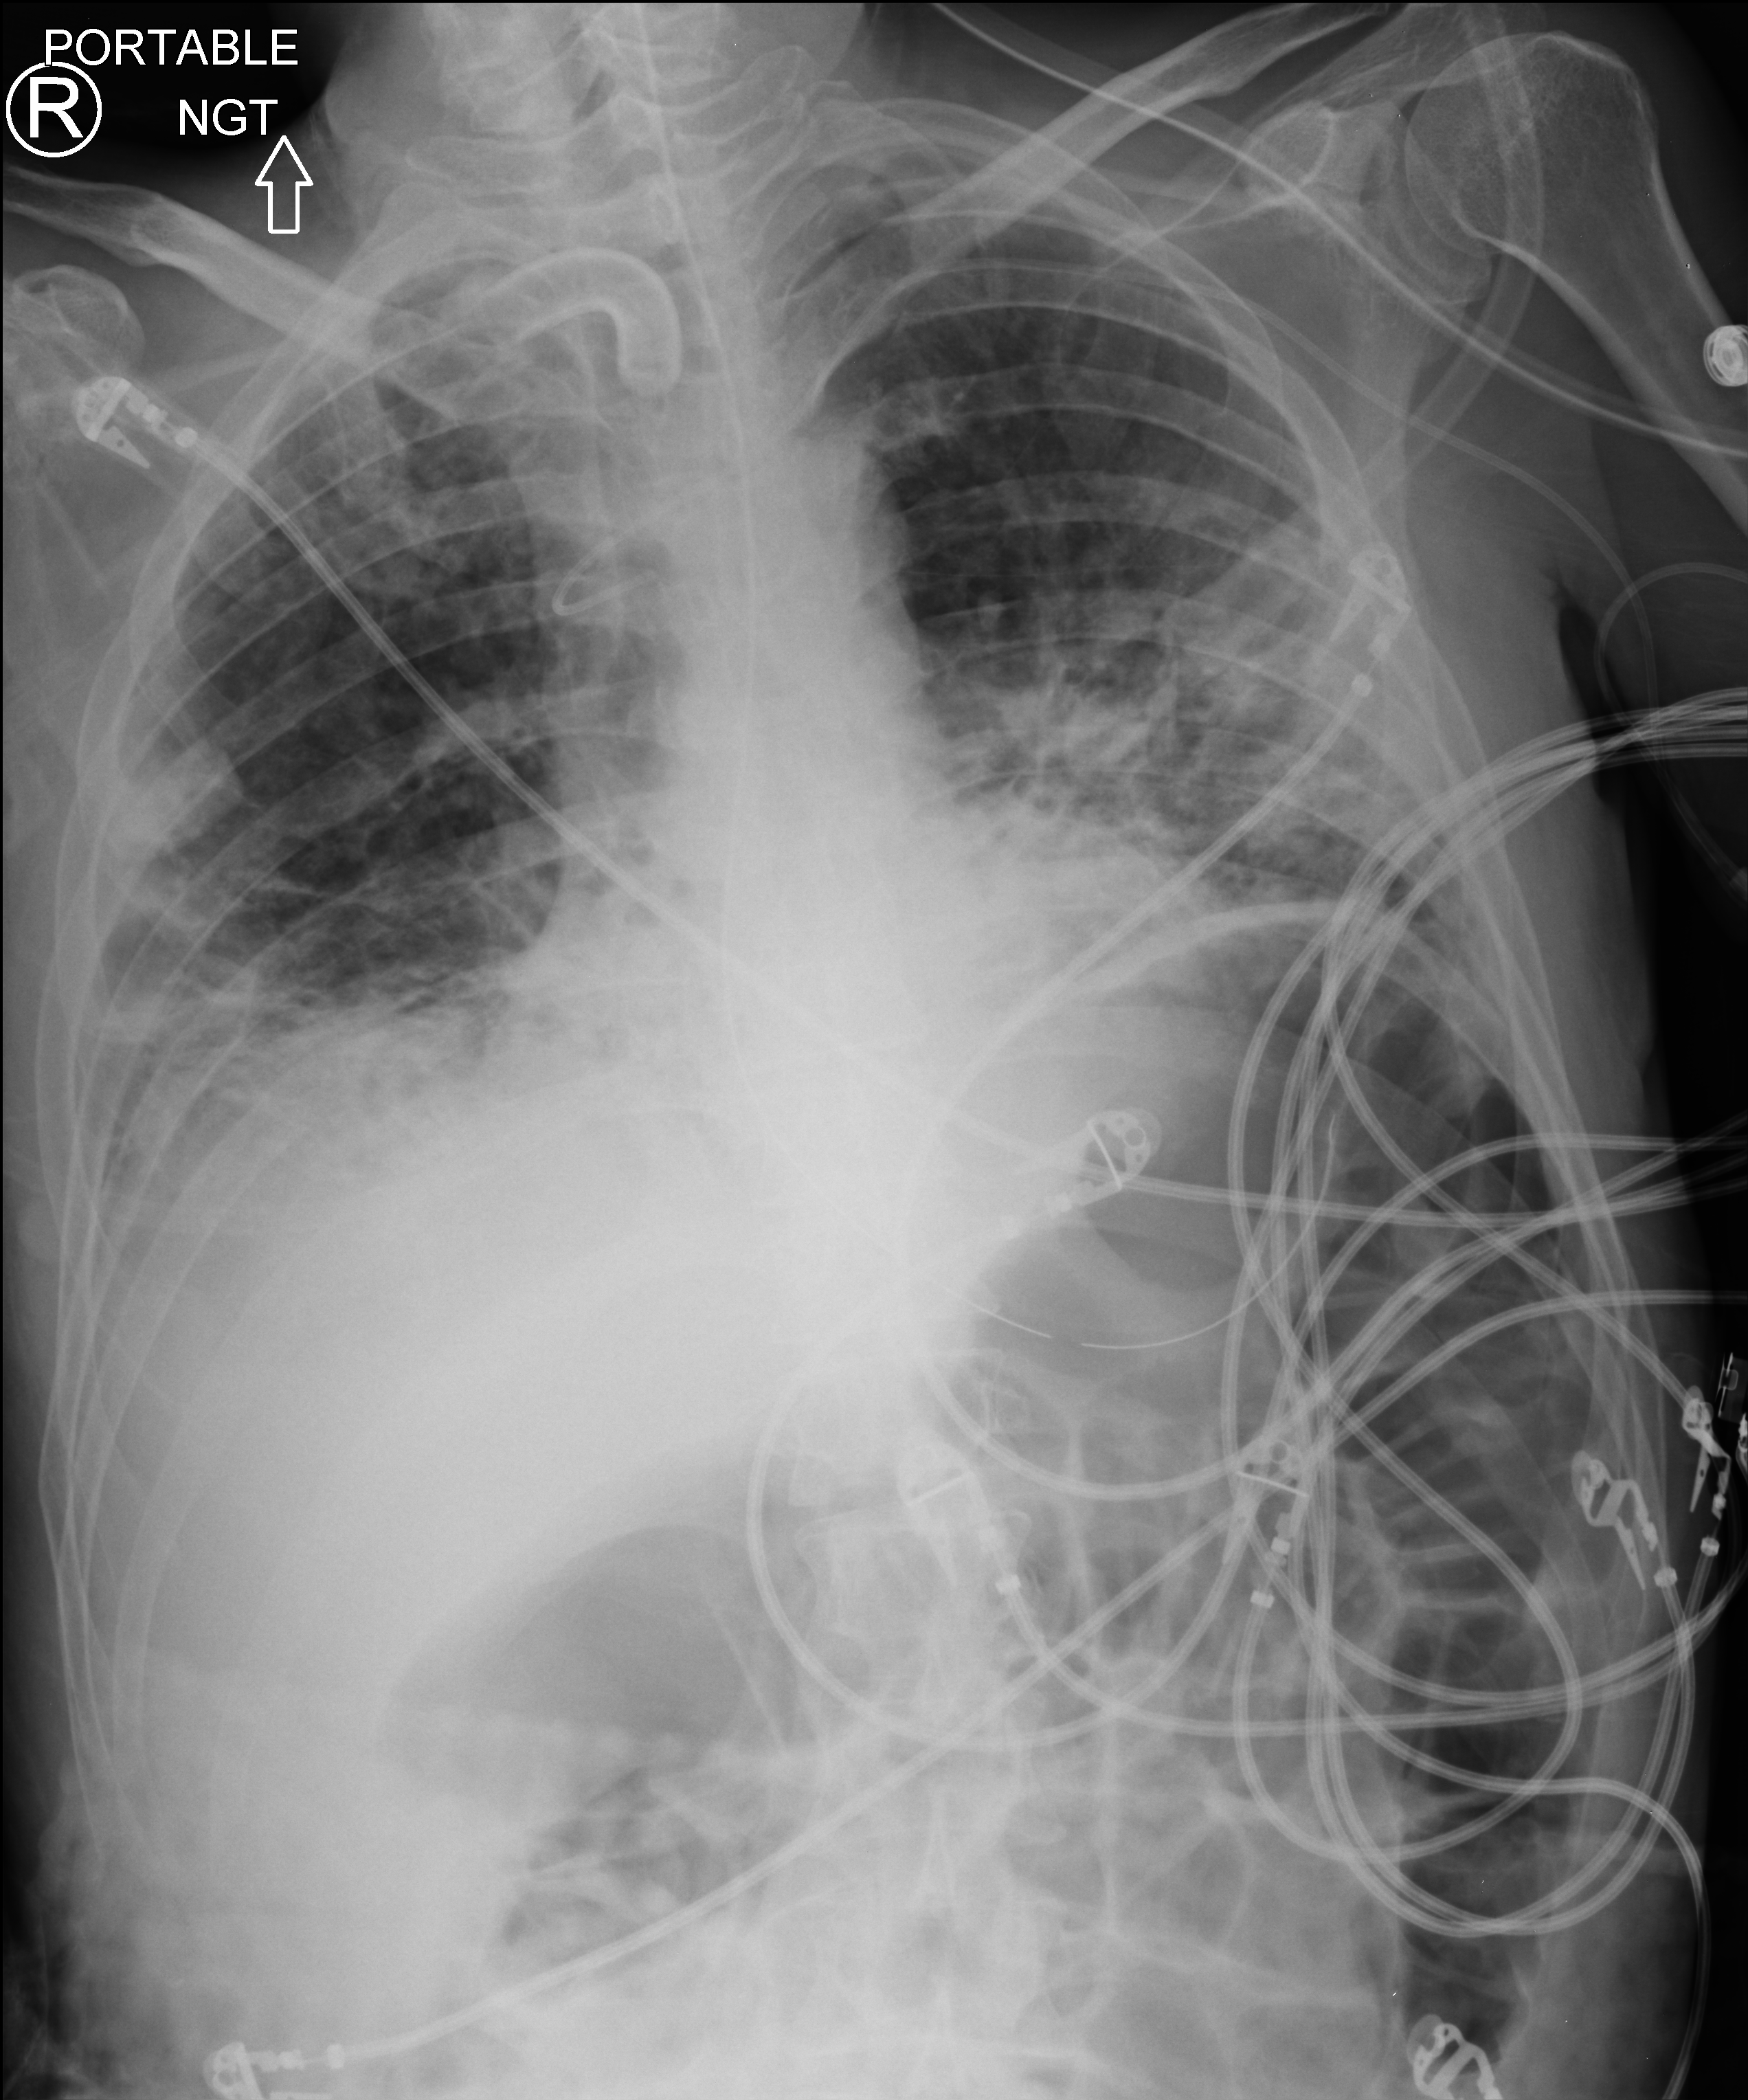
Portable chest radiograph; anteroposterior (AP) projection. Male patient hospitalised with COVID-19, age 18–59 years.
Hospital-stay facts (about this admission, not read from this image; timing relative to this image not recorded): mechanically ventilated during this hospital stay: yes; hypertension (admission record): yes; length of hospital stay: 96 days.